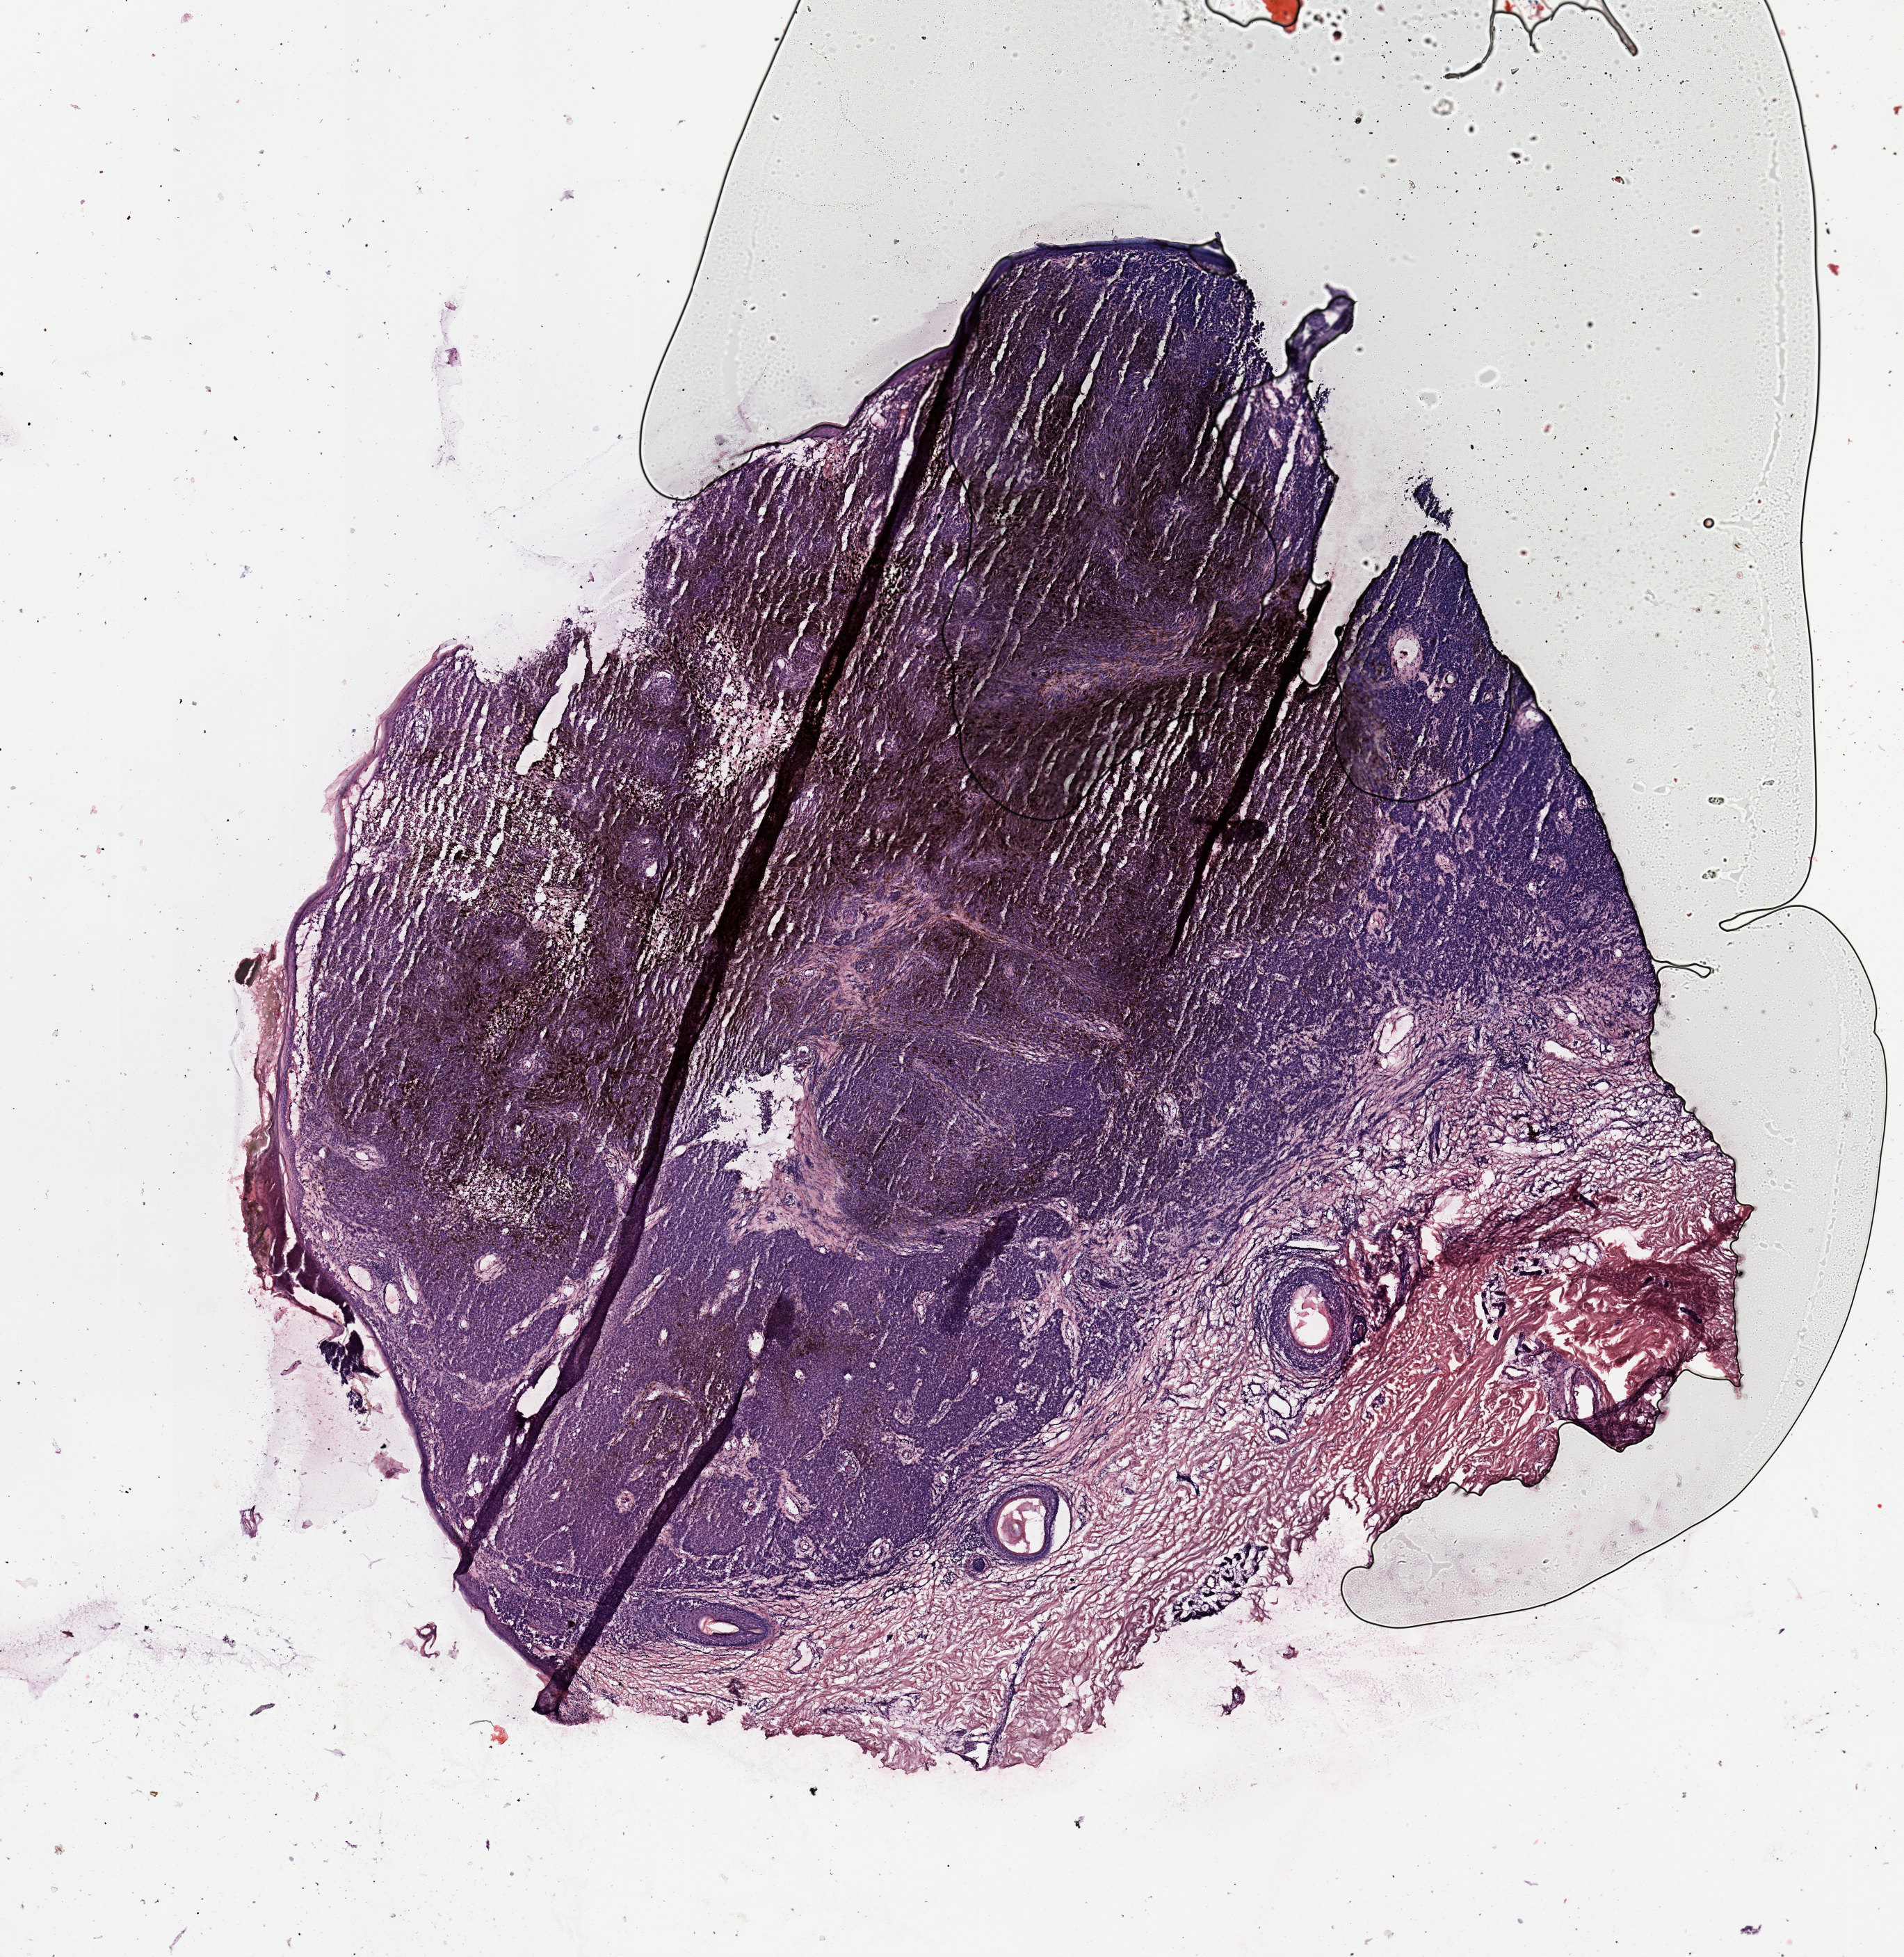
Whole-slide histology image, H&E — shown as a low-resolution overview of the whole scanned area (about 10.8 x 11.1 mm, slide scanned at 20x), melanoma tumour tissue; sampled site not recorded. Female, 53 y/o.
Primary tumour site (as recorded): trunk. Patient diagnosis (cohort enrolment): cutaneous melanoma (skin).